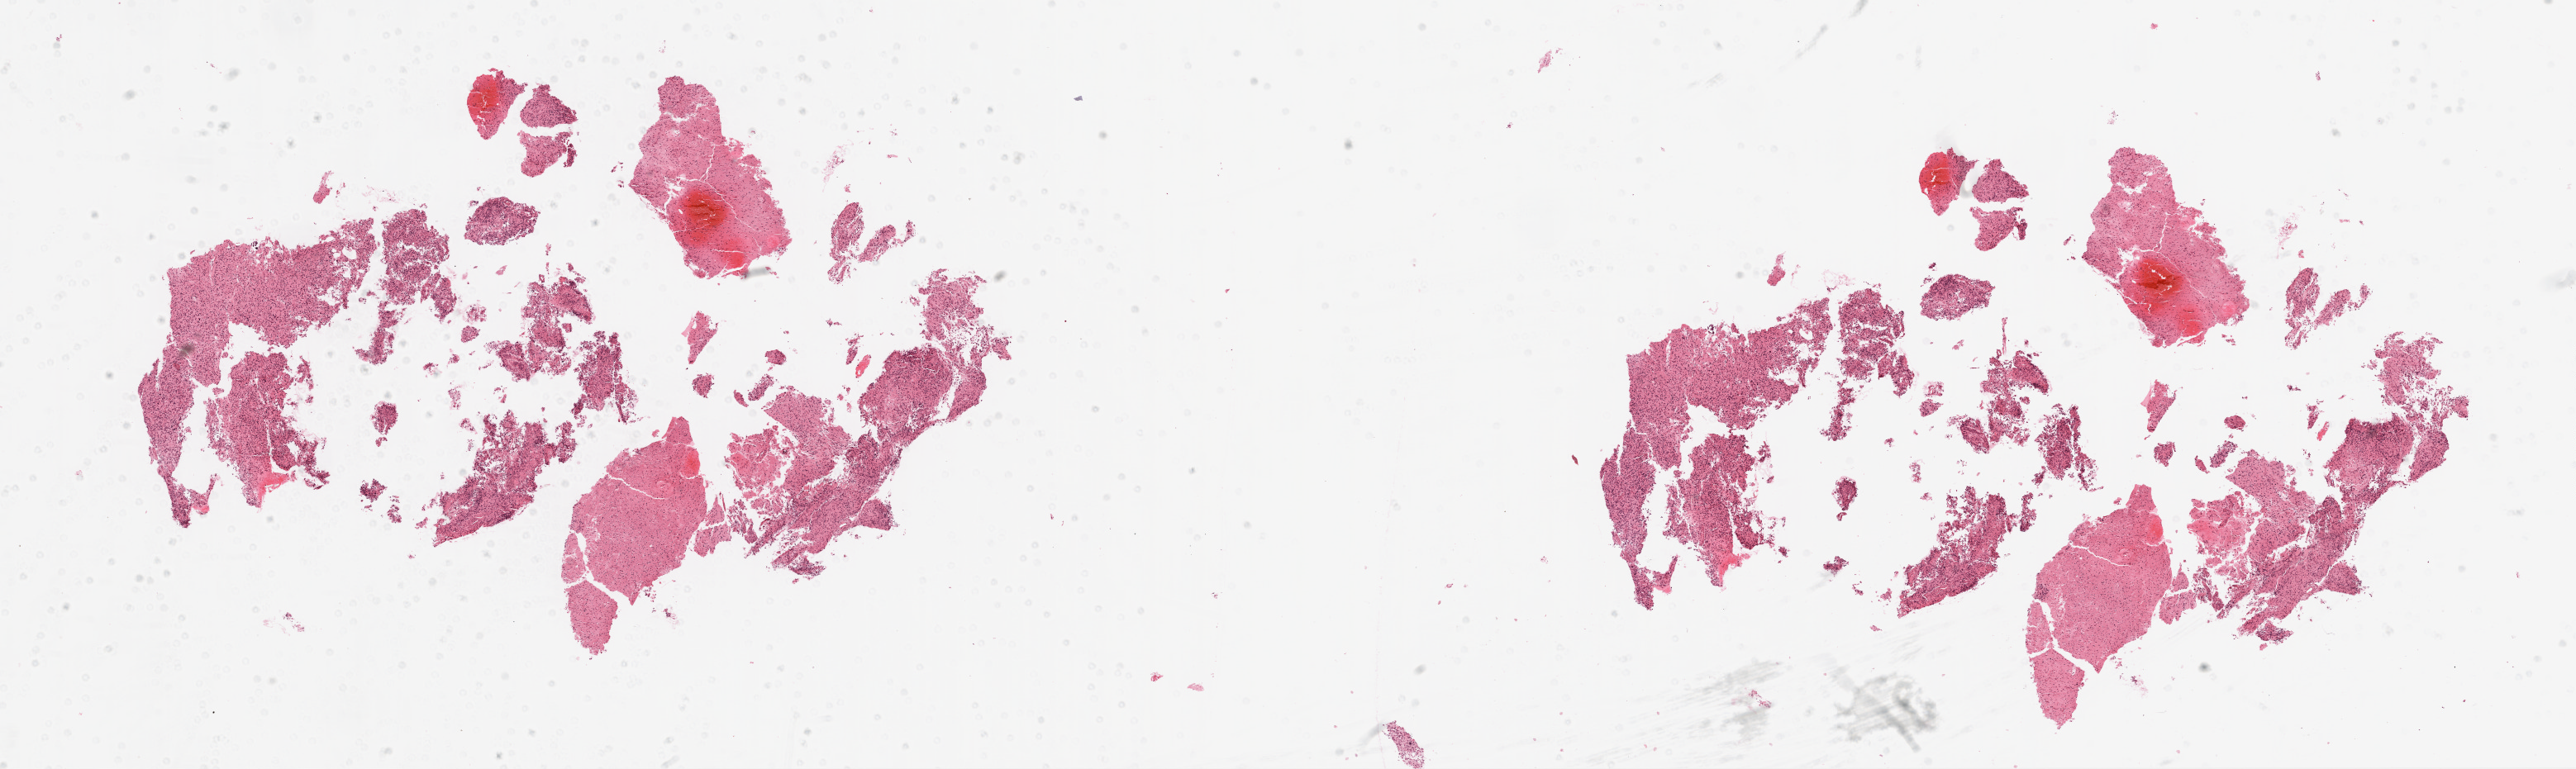
Whole-slide histology image, Hematoxylin and eosin (H&E) stained, shown as a low-resolution overview of the whole scanned area (about 25.1 x 7.5 mm, from a 20x scan); formalin-fixed paraffin-embedded (FFPE) diagnostic section; brain, primary tumour sample. Patient: male, age at initial diagnosis 77 years.
Pathologic diagnosis: Glioblastoma.